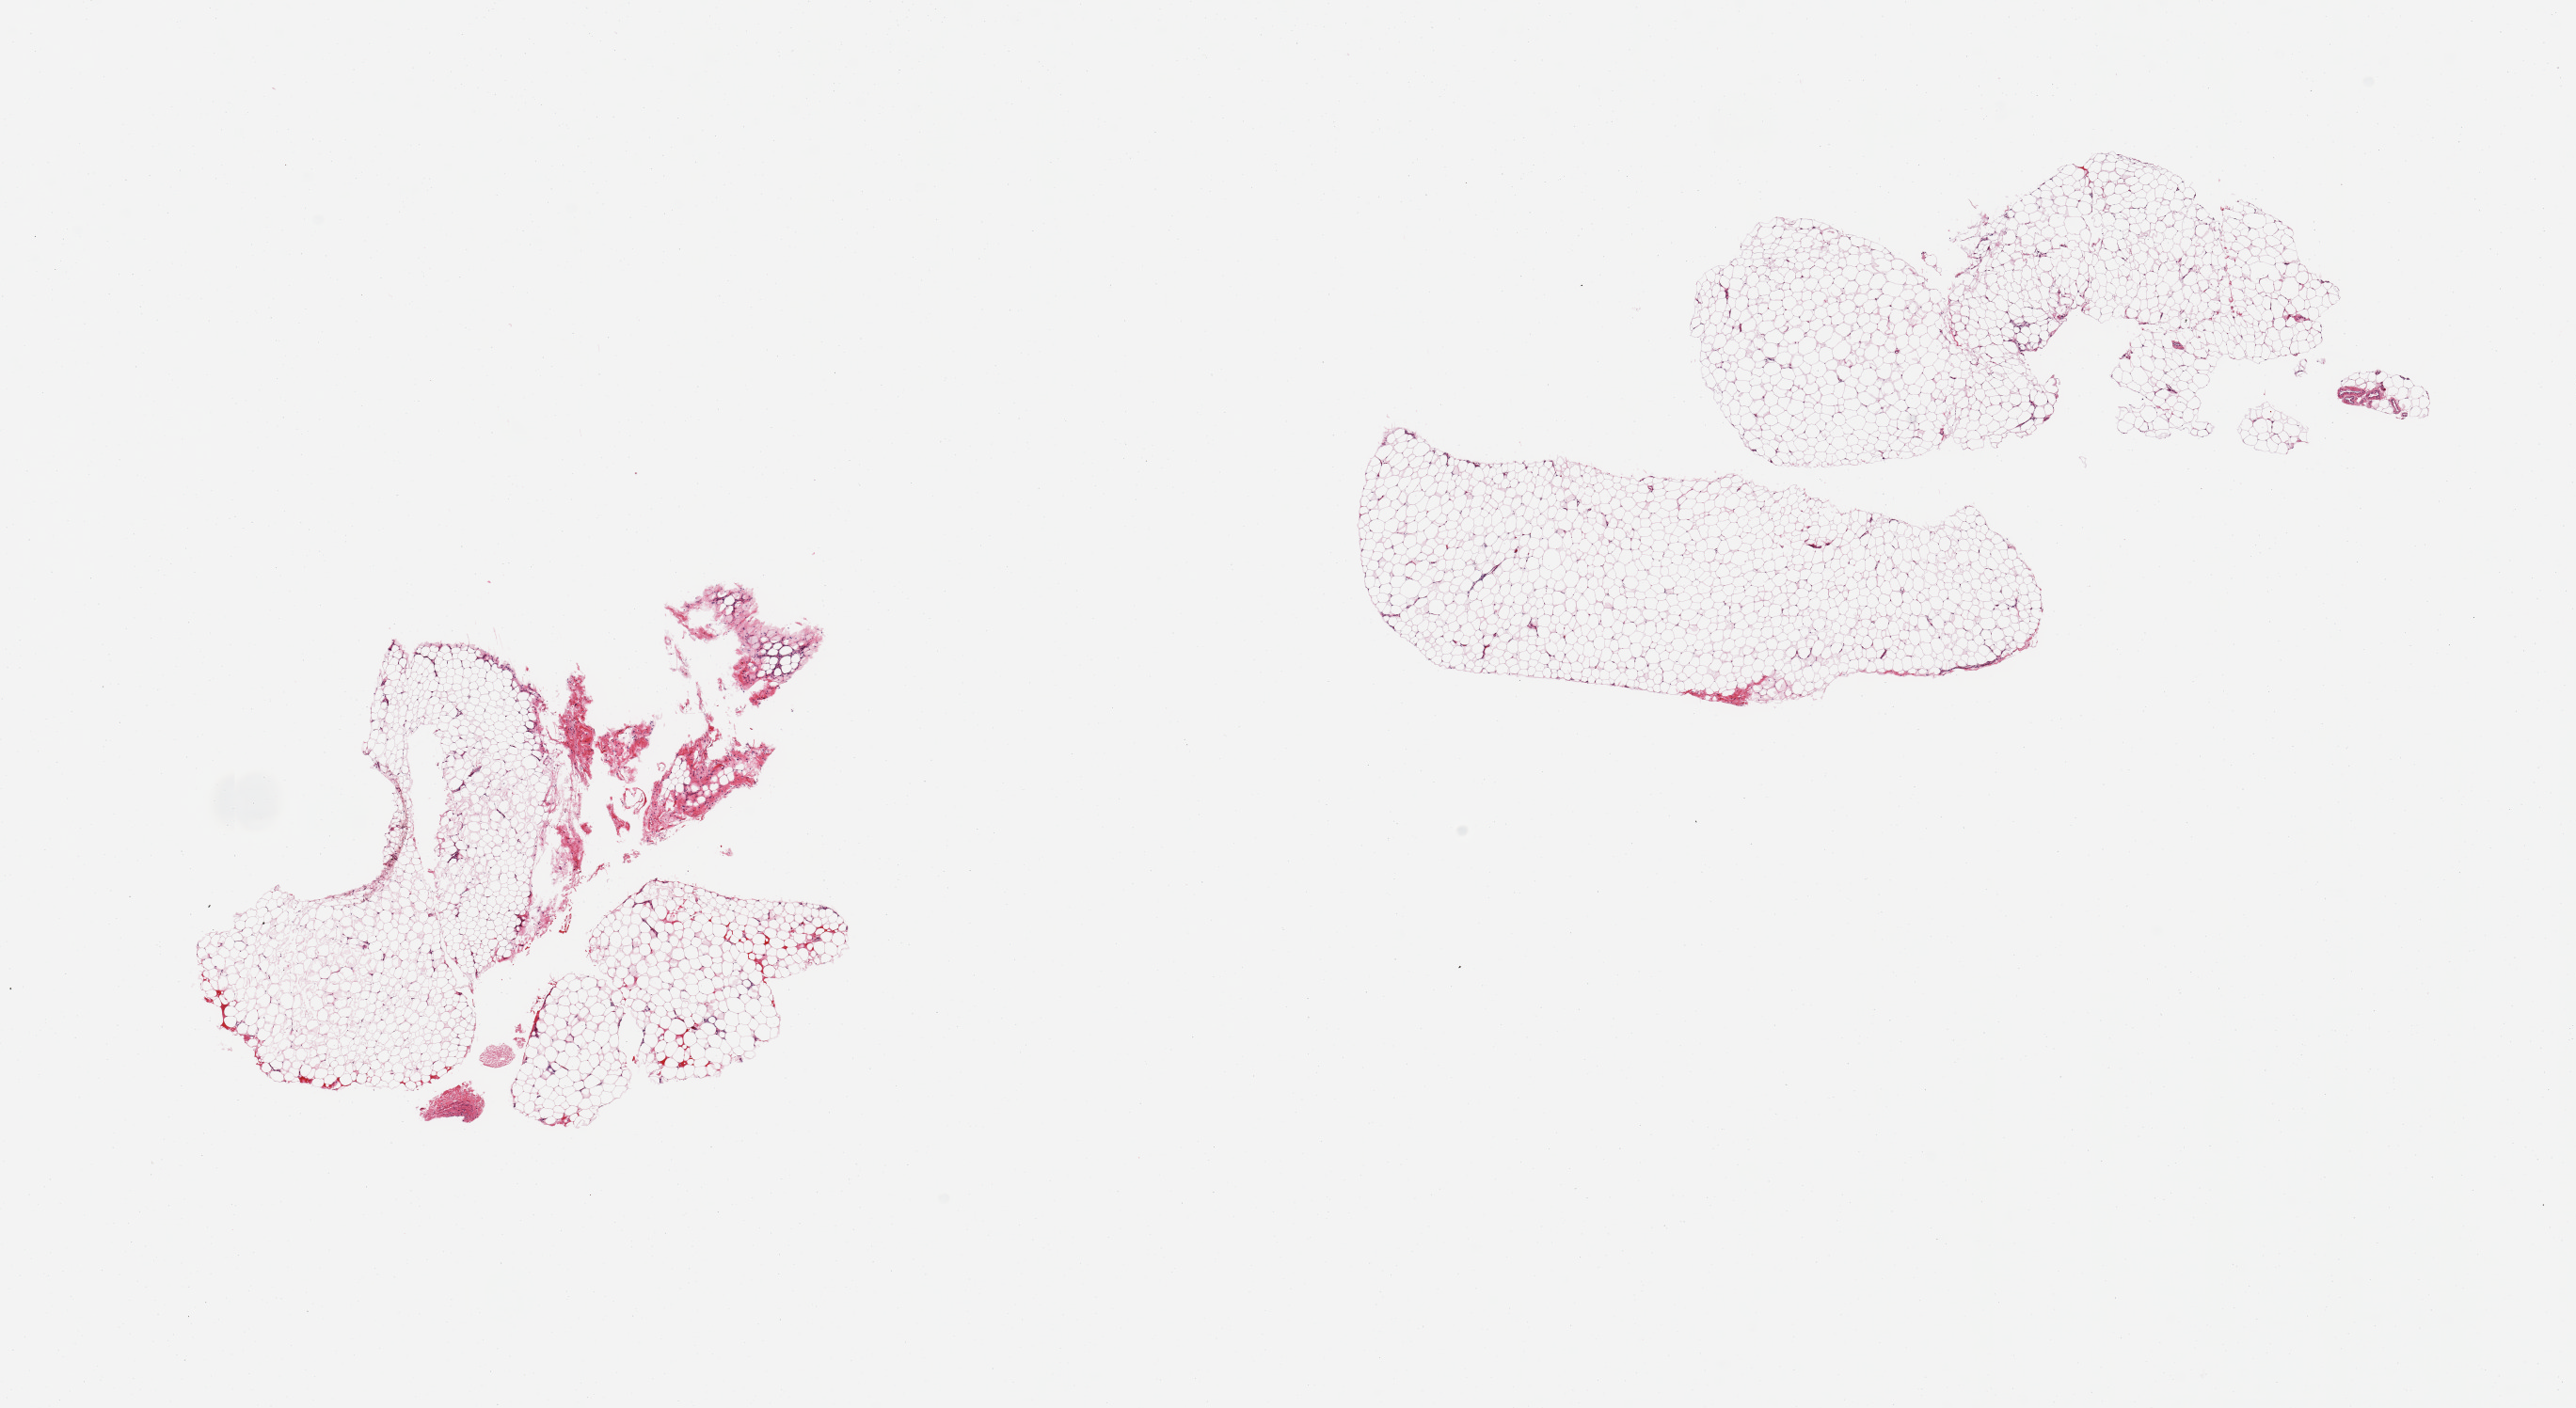
Whole-slide image, haematoxylin and eosin stain, brightfield, low-resolution overview of the scanned area, about 21.7 x 11.8 mm (acquisition: 20x scan). PAXgene-fixed, paraffin-embedded tissue. Section of adipose tissue (target tissue). Donor tissue sample. Donor: male.
Pathologist's review note for this sample: 2 pieces, ~10% fascia.